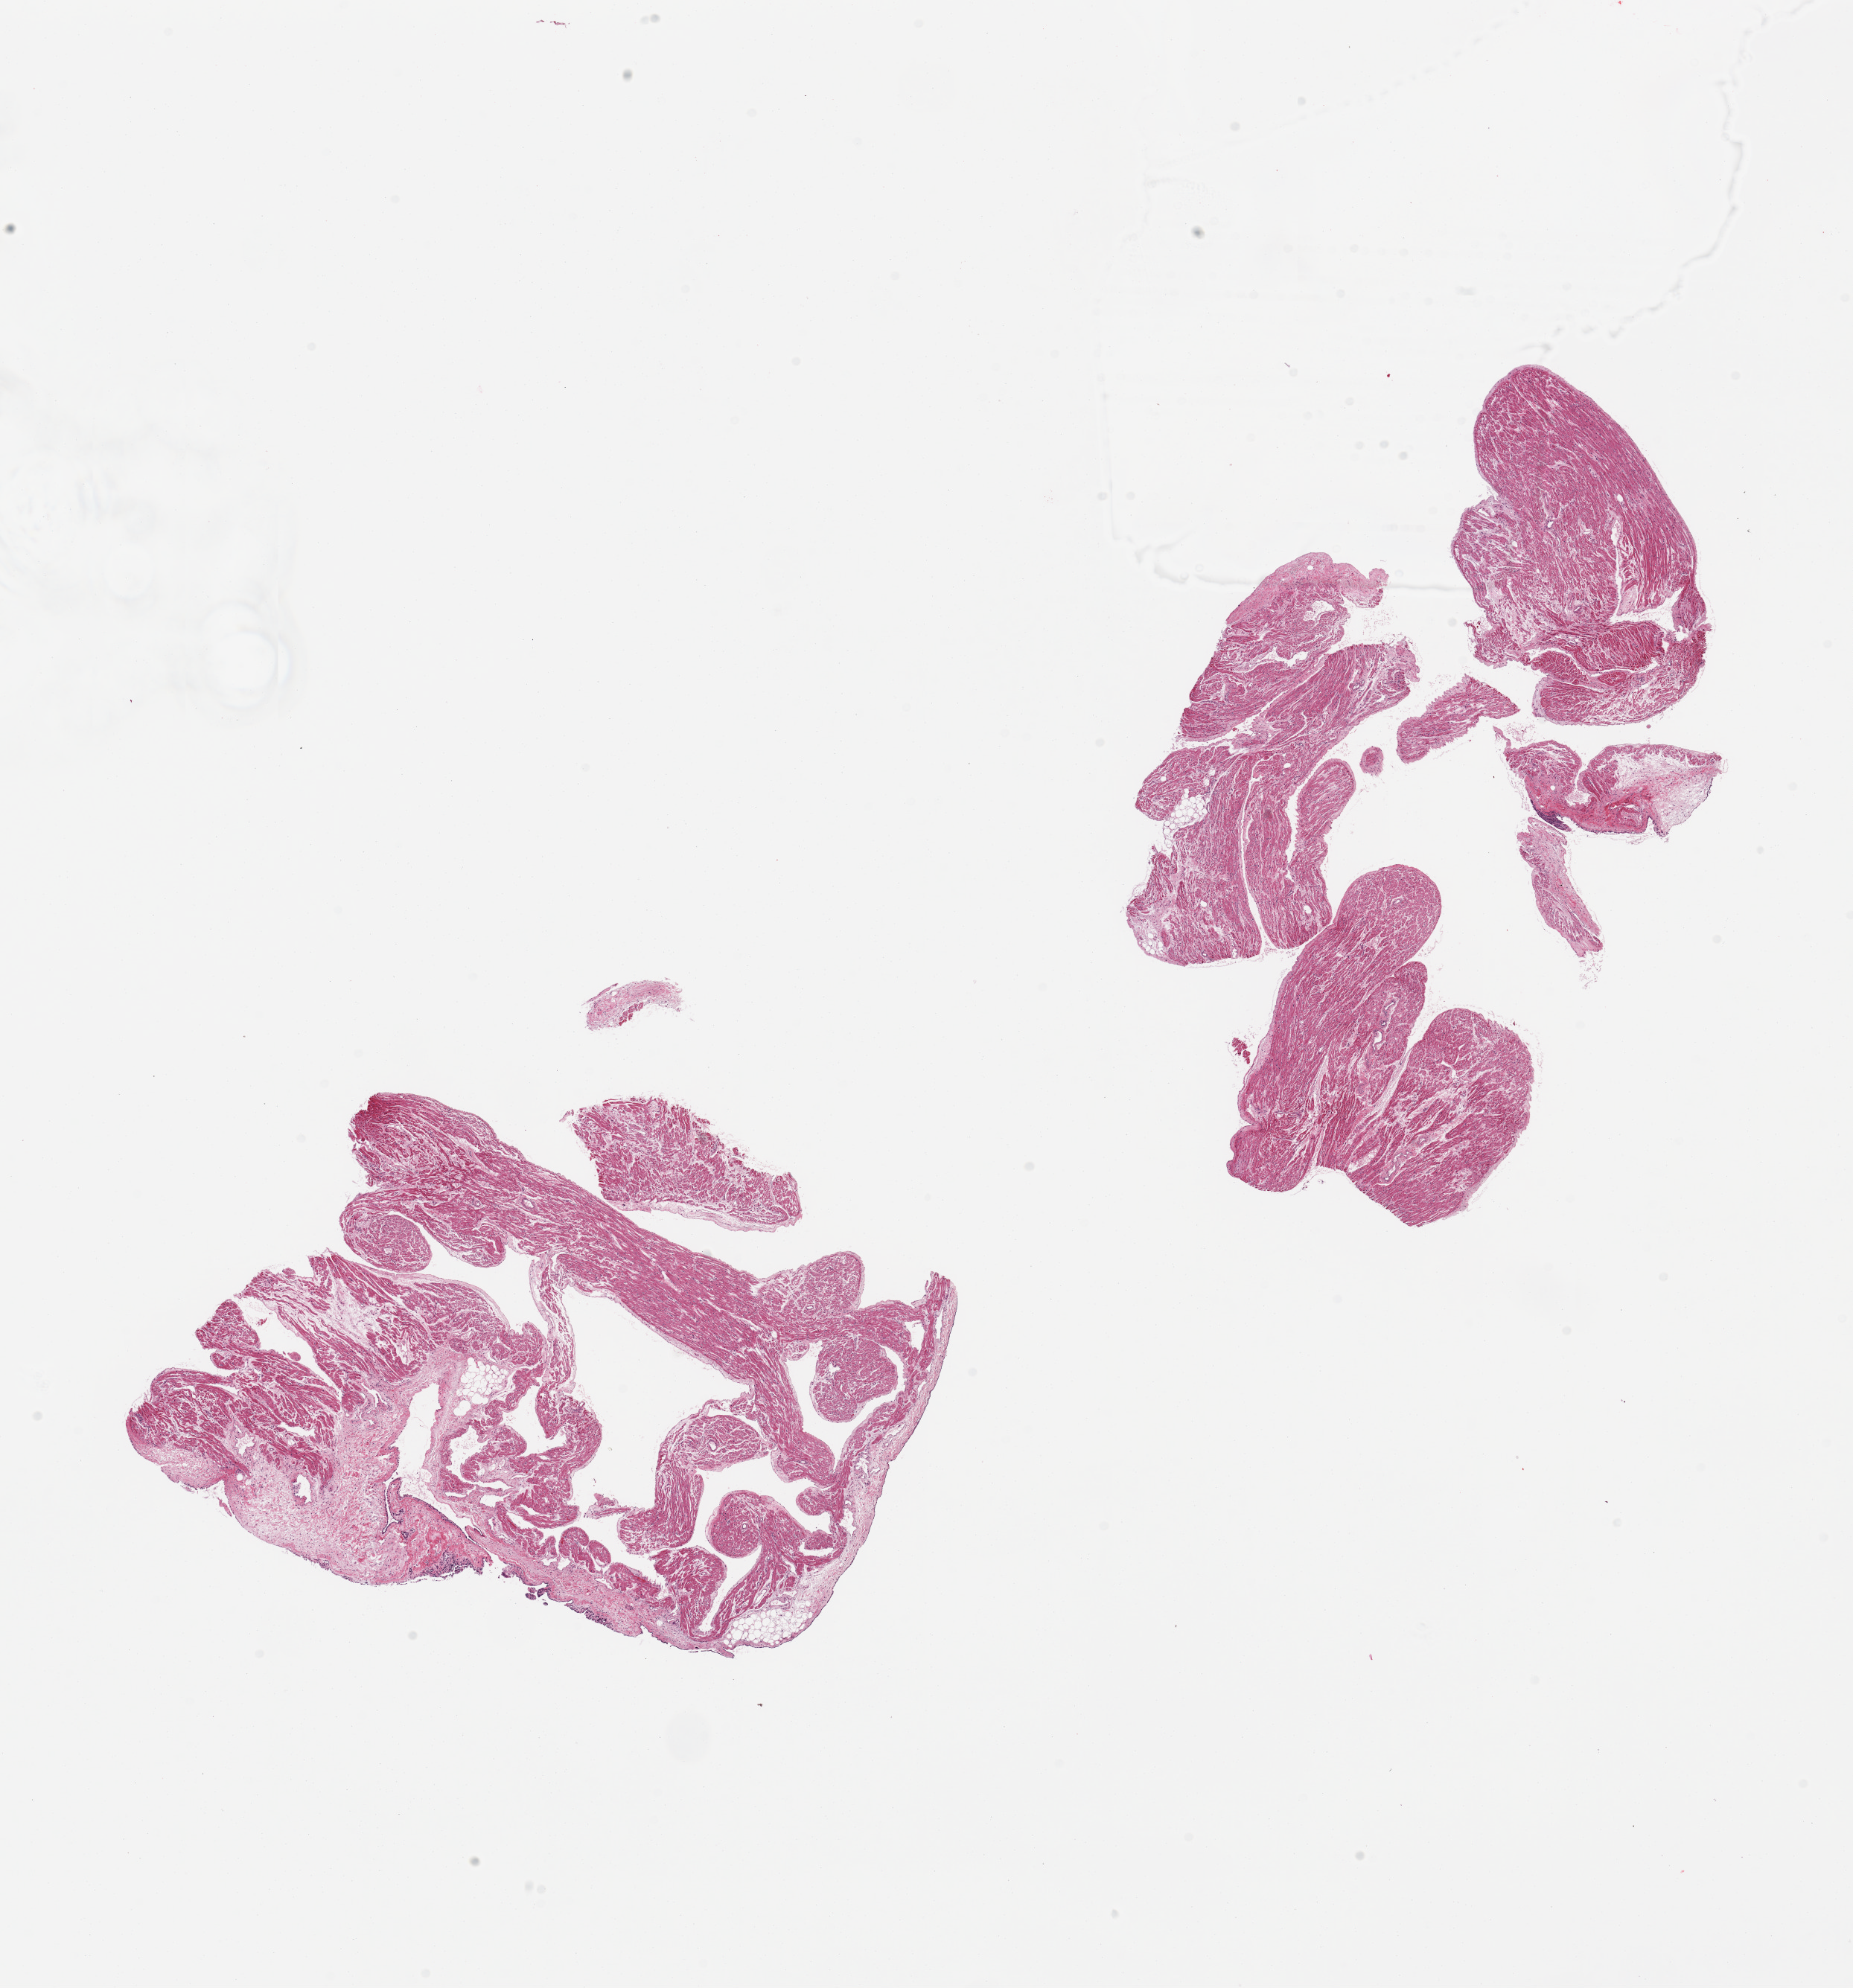
Digitized haematoxylin and eosin-stained section, brightfield, whole scanned area (about 19.7 x 21.1 mm) shown as a low-resolution overview. PAXgene-fixed, paraffin-embedded tissue. Target tissue: auricular appendage. Donor tissue sample.
- reviewer comment on this tissue sample: 2 pieces; 30% non-muscular stroma